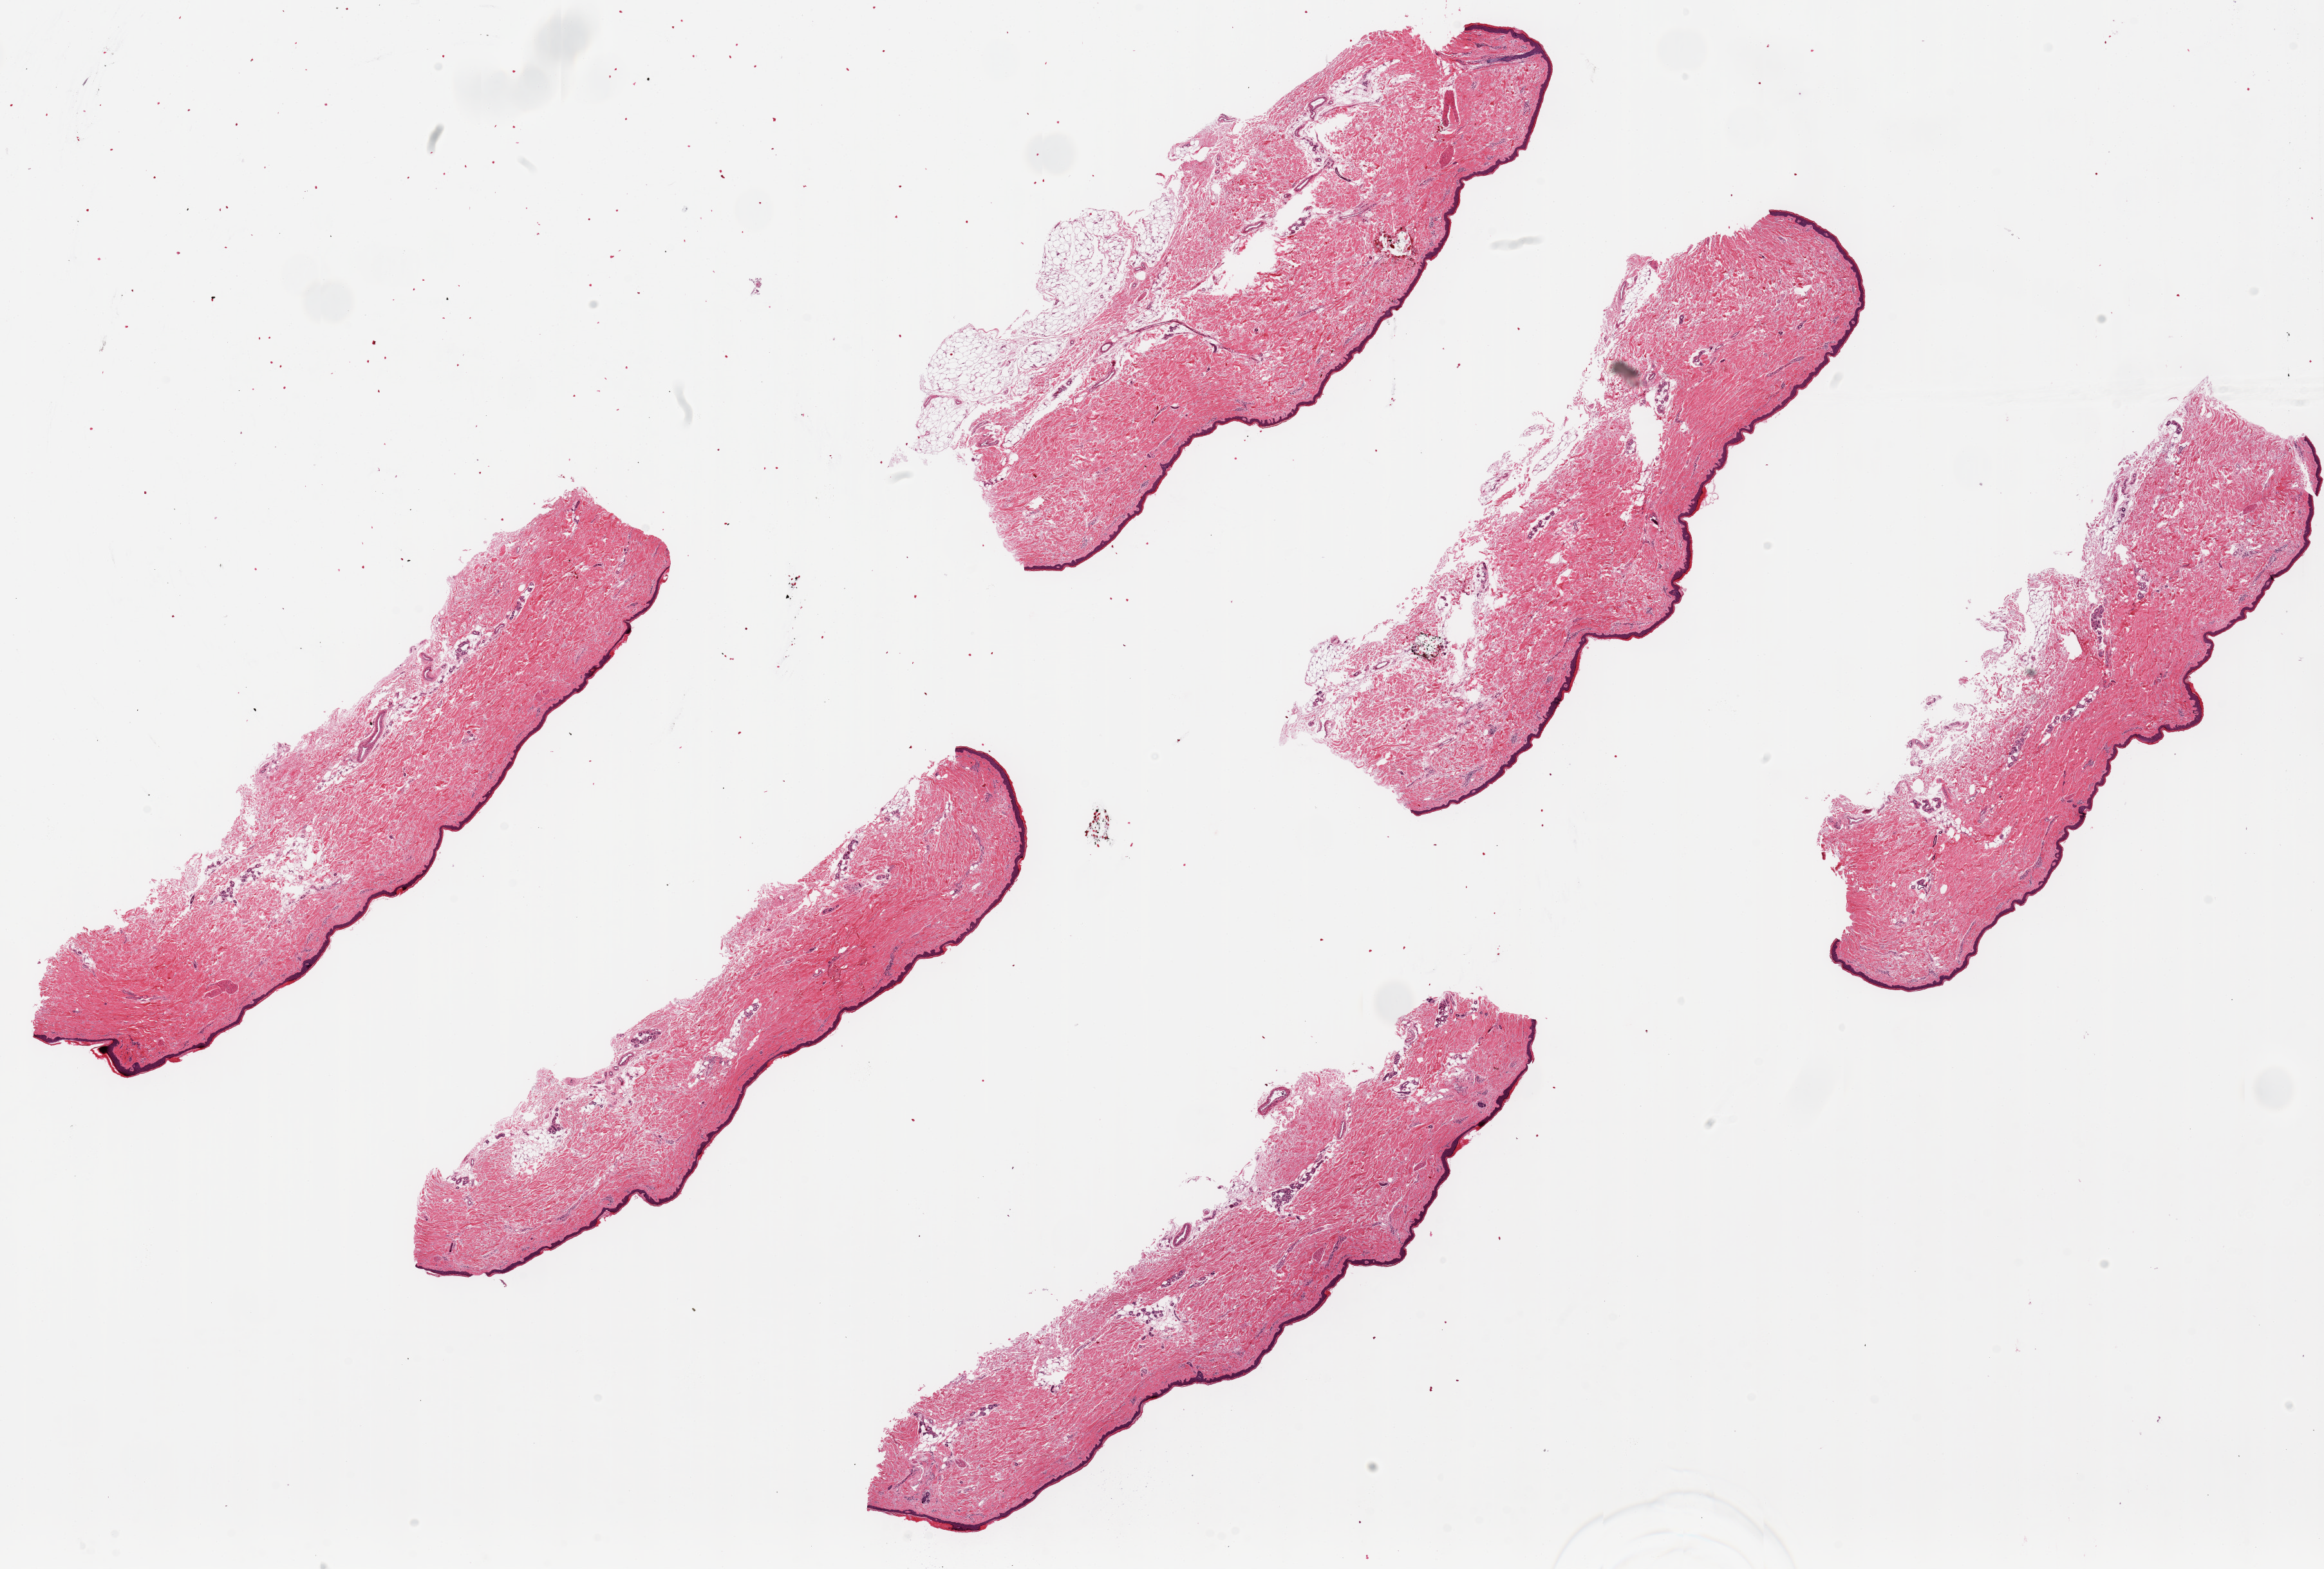
H&E whole-slide image, whole scanned area (about 28.5 x 19.3 mm, from a 20x scan) shown as a low-resolution overview; PAXgene-fixed paraffin-embedded (PFPE) section; section of skin of lower leg (target tissue); donor tissue sample.
* reviewer comment on this tissue sample: 6 ~9x1.5mm pieces. Squamous epithelium is ~2-3% of thickness